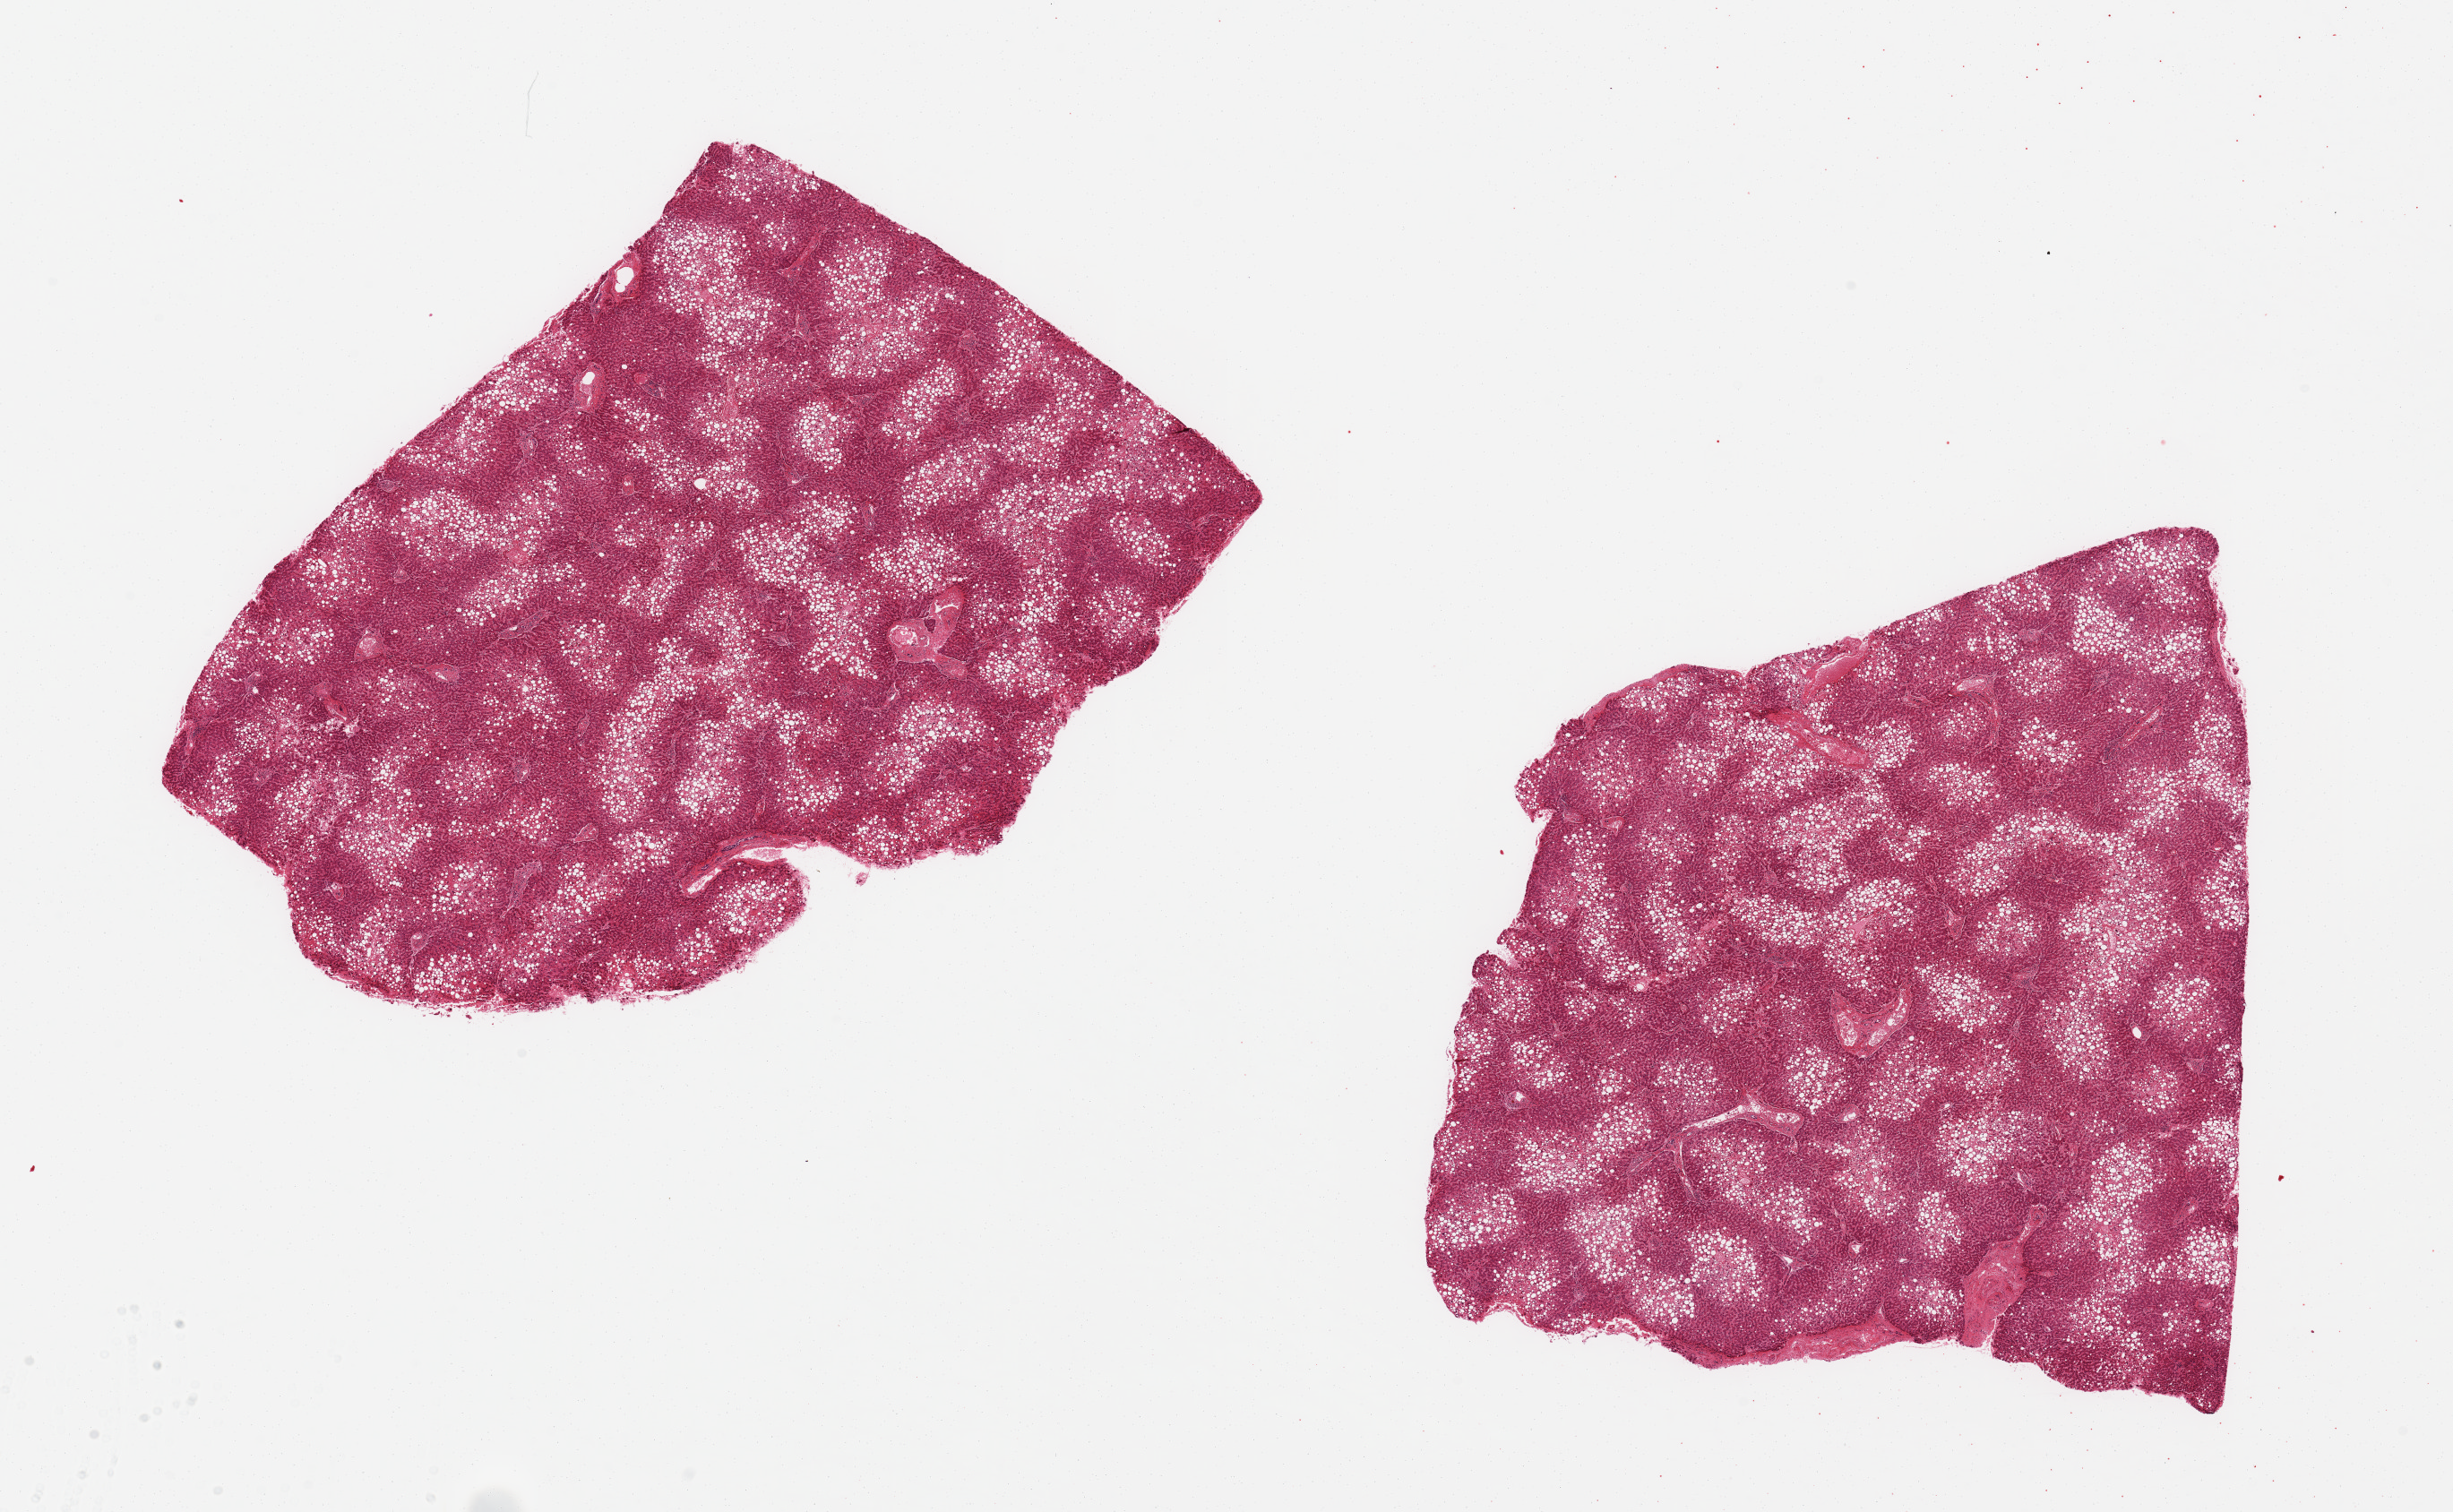
Haematoxylin and eosin whole-slide image — shown as a low-resolution overview of the whole scanned area (about 21.7 x 13.4 mm, acquisition: 20x scan); PAXgene-fixed, paraffin-embedded tissue; section of liver (target tissue); tissue donor sample. Donor: male.
Reviewer comment on this tissue sample: 2 aliquots, ~8x6mm. Diffuse macrovesicular steatosis involves ~70% of specimen.